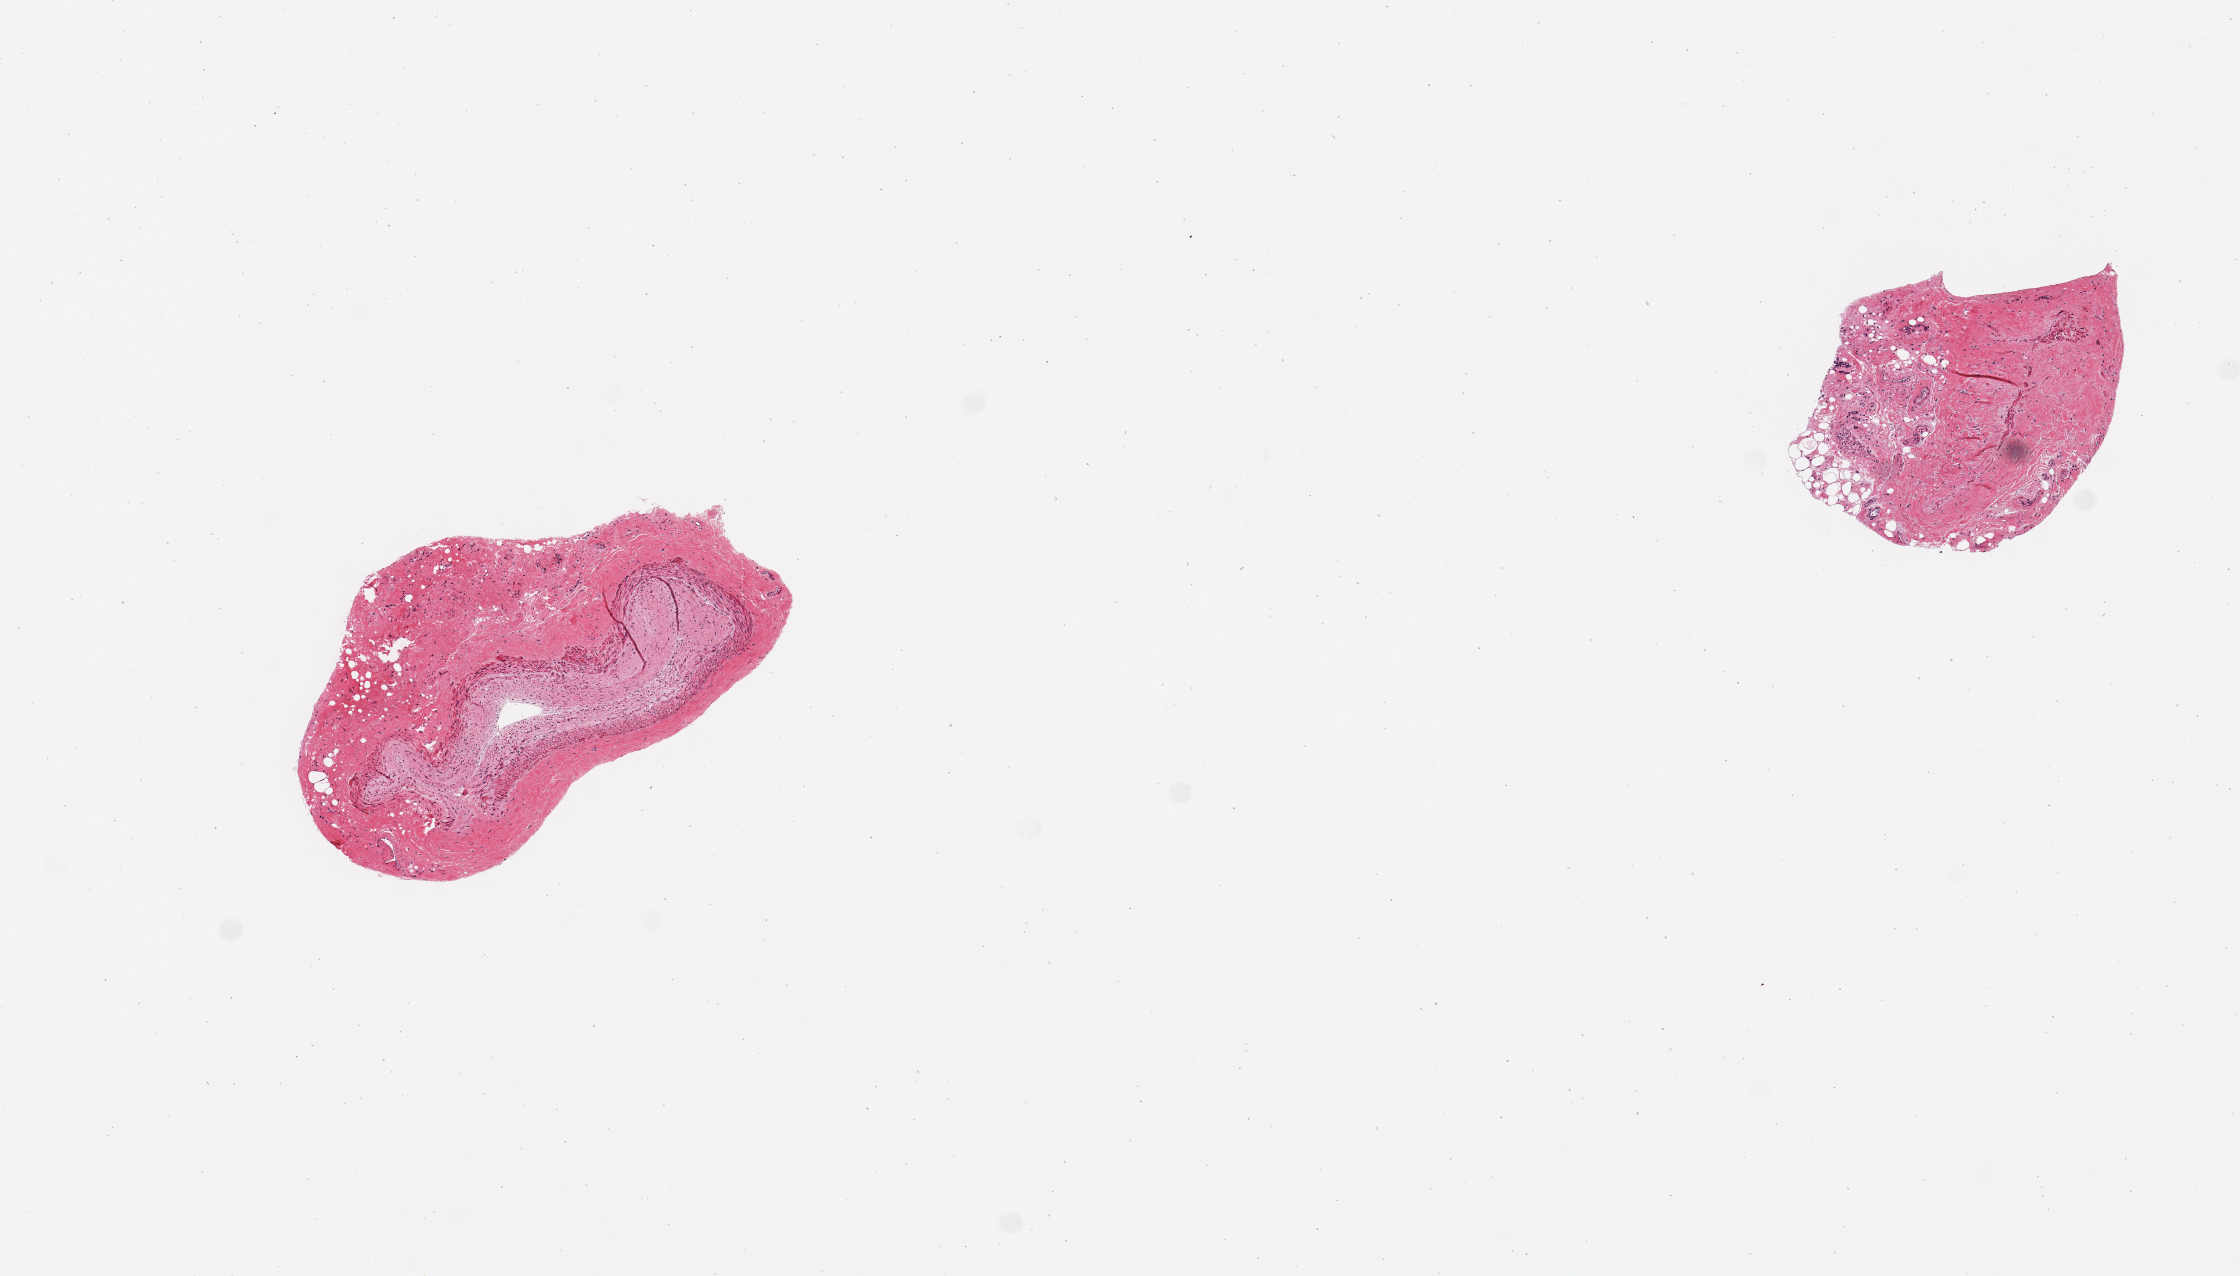
Haematoxylin and eosin whole-slide image, a low-resolution overview of the entire scanned area, about 8.9 x 5.0 mm (slide scanned at 20x). PAXgene-fixed paraffin-embedded (PFPE) section. Target tissue: coronary artery. Donor tissue sample. Donor: female.
Pathologist's review note for this sample: 2 pieces, compressed lumina; not visible atherosis.